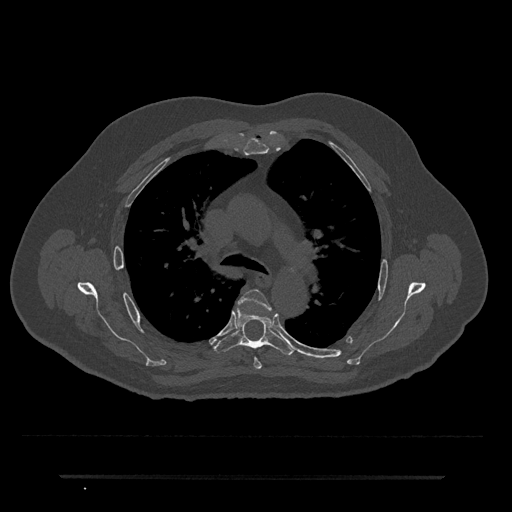
CT including the spine, one axial slice. Position 497 of 797 along the scan axis. Reconstruction kernel Br40s/3. 120 kVp. Bone window (W 1800 / L 400 HU). 0.5 mm slice thickness. 512 × 512 image matrix, field of view 437 × 437 mm. Patient: male, 69 years. From the clinical record (not read from this slice): primary cancer: prostate.
Annotated regions visible in this slice (semi-automatically segmented with operator editing):
- T4 vertebra: bounding box <239,289,271,369> (left, top, right, bottom; pixels)
- T5 vertebra: <213,308,295,355>